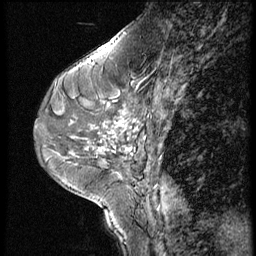
Breast MRI (dynamic contrast-enhanced), one sagittal slice; slice 24 of 56 in the series (ordered by position); 3 images stored at this slice position (order not interpretable as contrast timing); 1.5 T; TE 4.2 ms, TR 9 ms; 2.5 mm slice thickness; 256 × 256 image matrix, field of view 180 × 180 mm. Female patient, age 46 years. From the clinical record (not read from this slice): setting: breast cancer imaged before/during neoadjuvant chemotherapy; receptor status: HER2-positive.
Structures marked on this image (semi-automatically segmented with operator editing):
- analysis volume of interest (the breast-tissue region the enhancement analysis was run in; not a lesion): bounding box (x1, y1, x2, y2) in pixels: (73, 86, 164, 161)
- tumour enhancement mask (voxels above the 140 % enhancement threshold inside the analysis volume of interest): (115, 122, 131, 150)